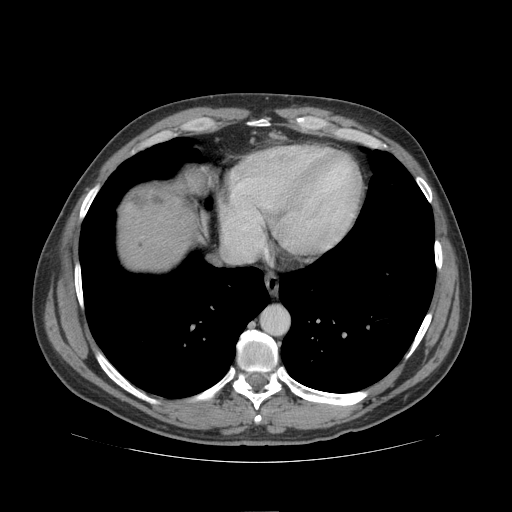
Contrast-enhanced abdominal CT (liver protocol), one axial slice. Position 96 of 109 along the scan axis. Reconstruction kernel STANDARD. Soft-tissue window (W 400 / L 40 HU). 2.5 mm slice thickness. 512 × 512 image matrix. Case-level facts recorded for this patient, not image findings: diagnosis: hepatocellular carcinoma (patient treated with transarterial chemoembolisation; whether this scan precedes or follows treatment is not stated here); TNM stage (as recorded): Stage-IIIB; Child-Pugh class: A.
Annotated regions visible in this slice (semi-automatically segmented with operator editing):
- liver parenchyma outside the tumour (the mass and vessels are separate outlines, so this box may not span the whole liver): bounding box [x1, y1, x2, y2] px = [118, 200, 196, 270]
- mass: [123, 169, 212, 221]